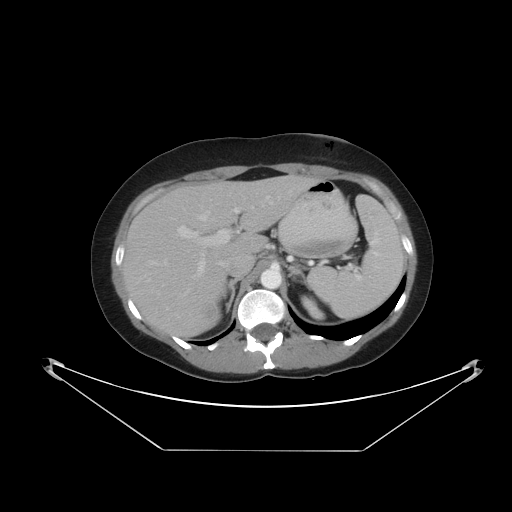
Contrast-enhanced abdominal CT, one axial slice. Position 30 of 48 along the scan axis. Reconstruction kernel STANDARD. 120 kVp. Intravenous contrast given. Soft-tissue window (W 400 / L 40 HU). 5 mm slice thickness. 512 × 512 image matrix, field of view 482 × 482 mm. Female patient, age 38 years. From the clinical record (not read from this slice): diagnosis: colorectal cancer liver metastases, imaged before liver resection; multiple liver metastases: yes; largest metastasis: 2.5 cm; disease in both lobes: no.
Structures marked on this image (outlined manually by an expert reader):
- hepatic veins: bounding box <165,193,246,264> (left, top, right, bottom; pixels)
- liver: <121,175,314,339>
- planned liver remnant (the part of the liver to remain after resection): <167,176,306,253>
- portal vein (with intrahepatic branches): <178,196,273,277>